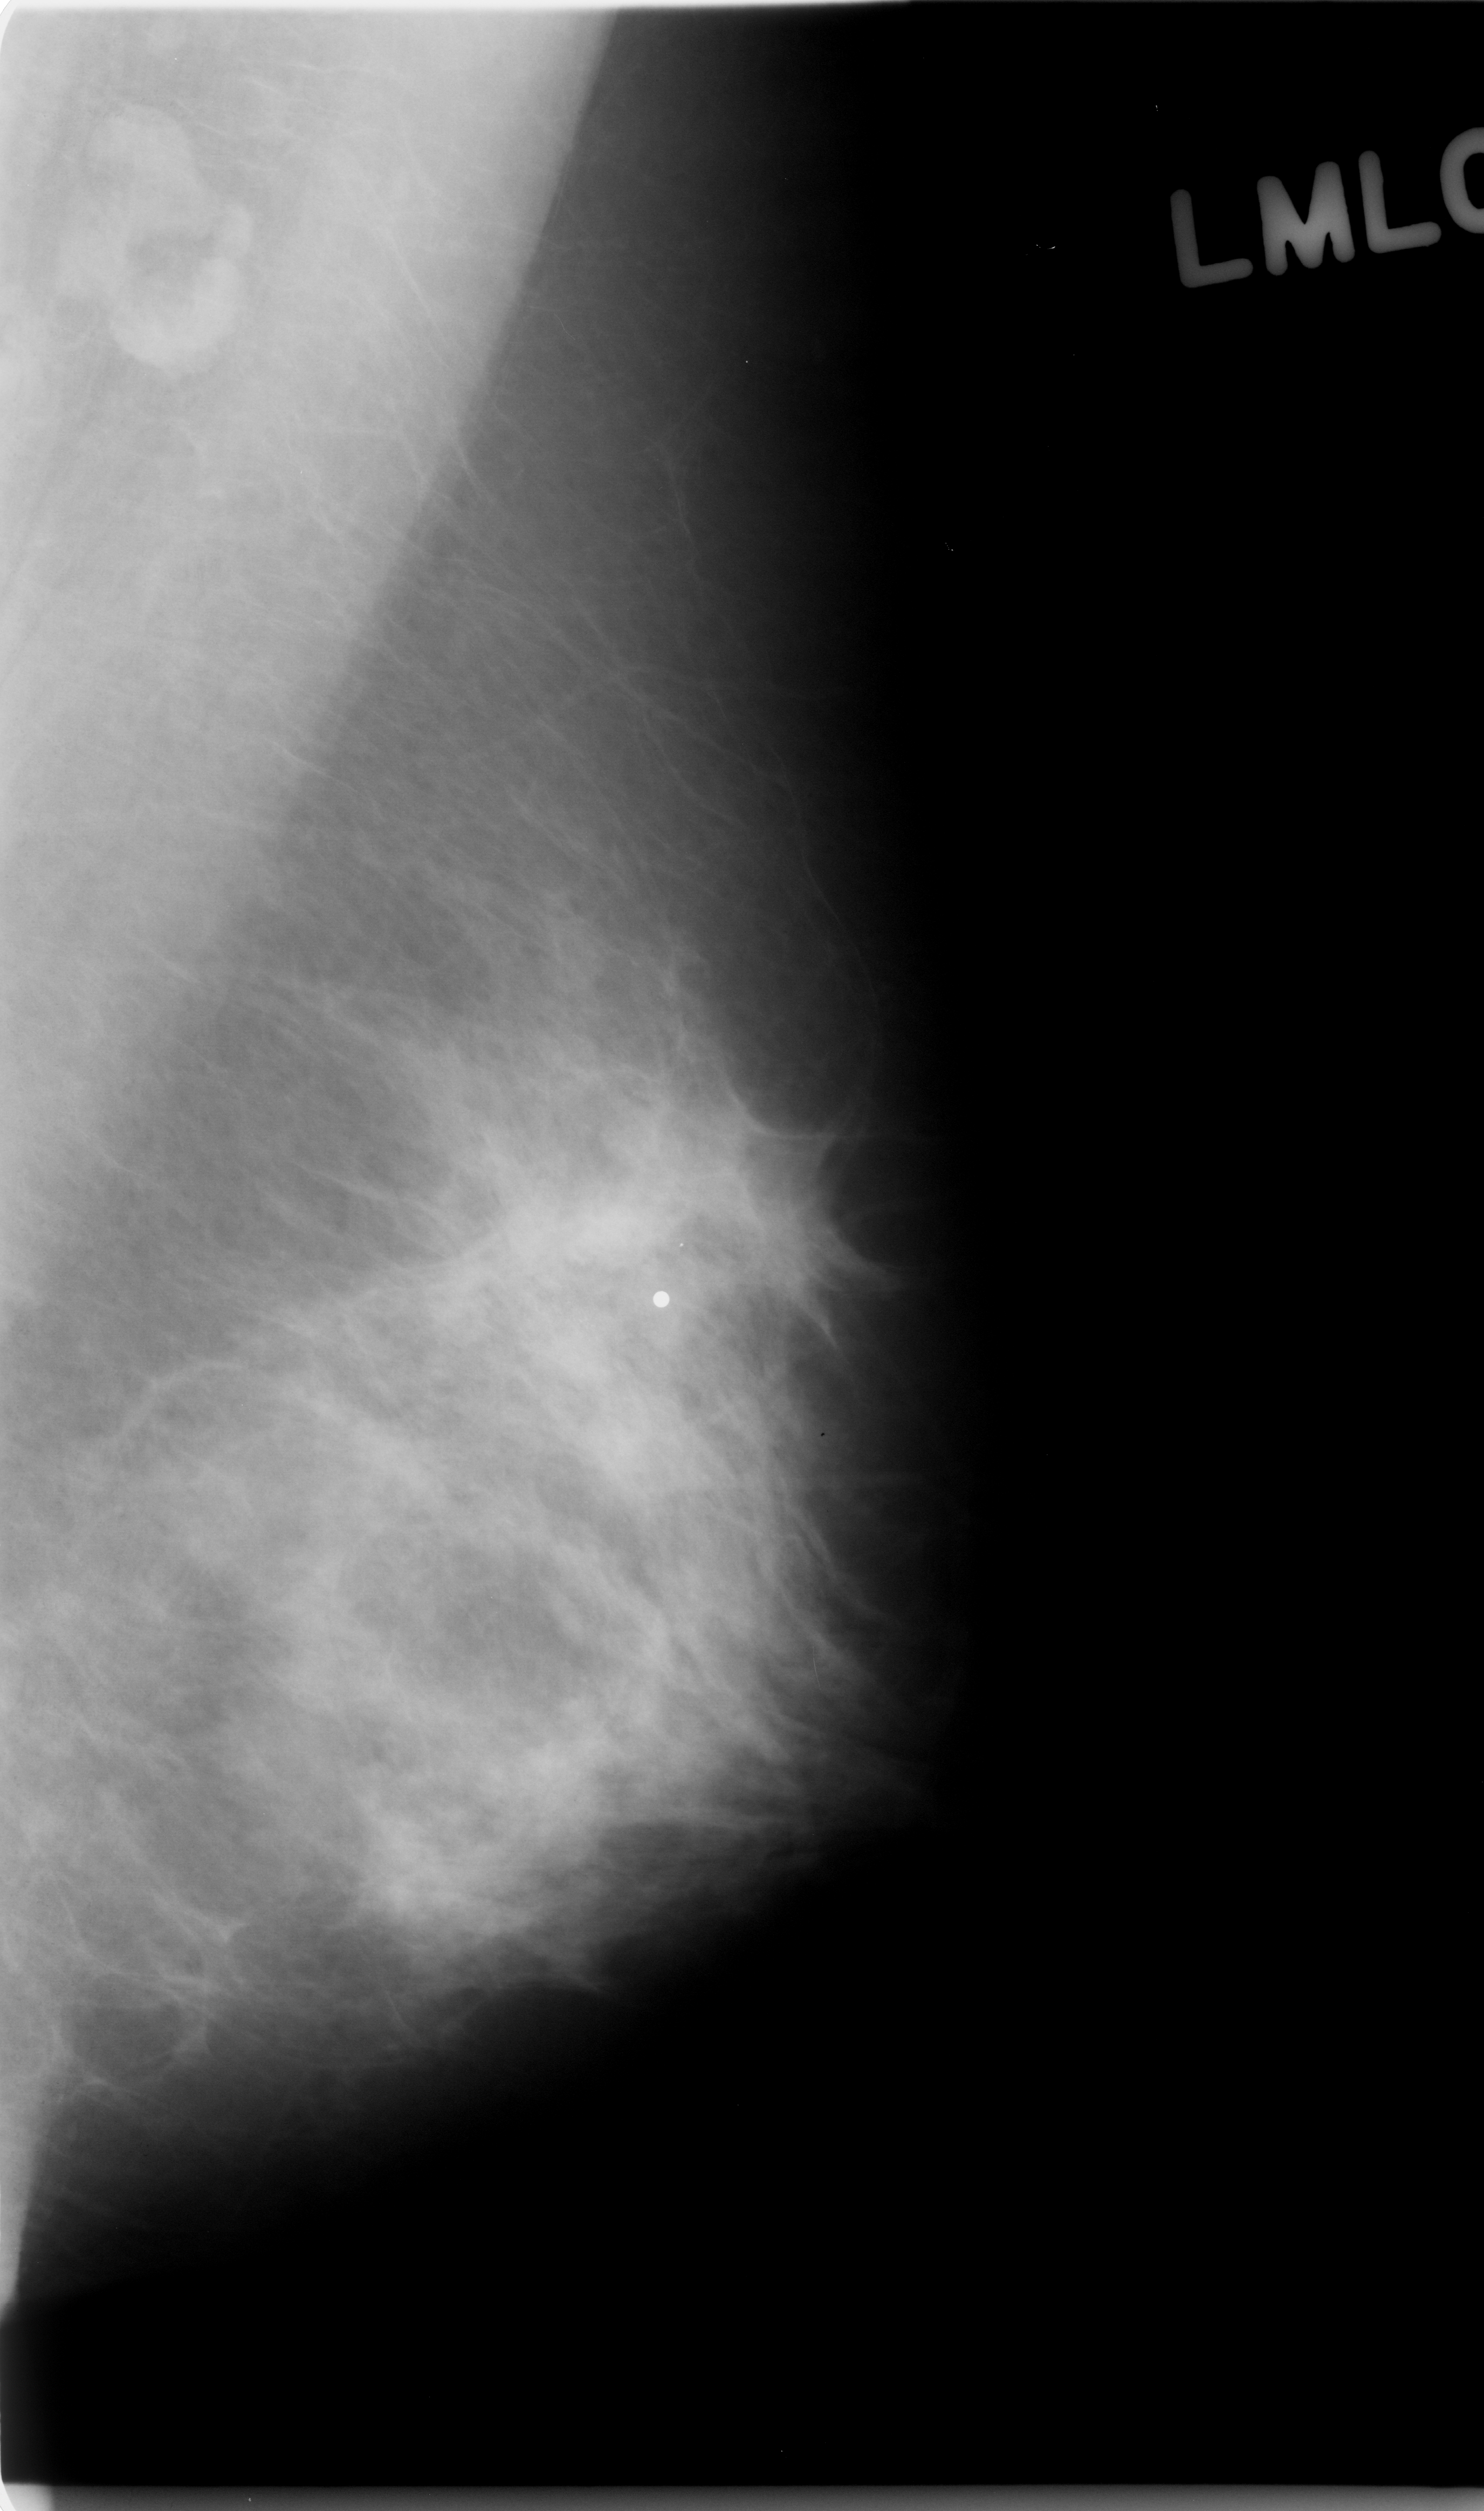
Mammogram (digitized film), left breast, mediolateral oblique (MLO) view.
Abnormality record for this image: calcifications, morphology amorphous, distribution clustered; BI-RADS assessment category 4; subtlety rating 2 on a 1 (subtle) to 5 (obvious) scale; pathology (as recorded): malignant.